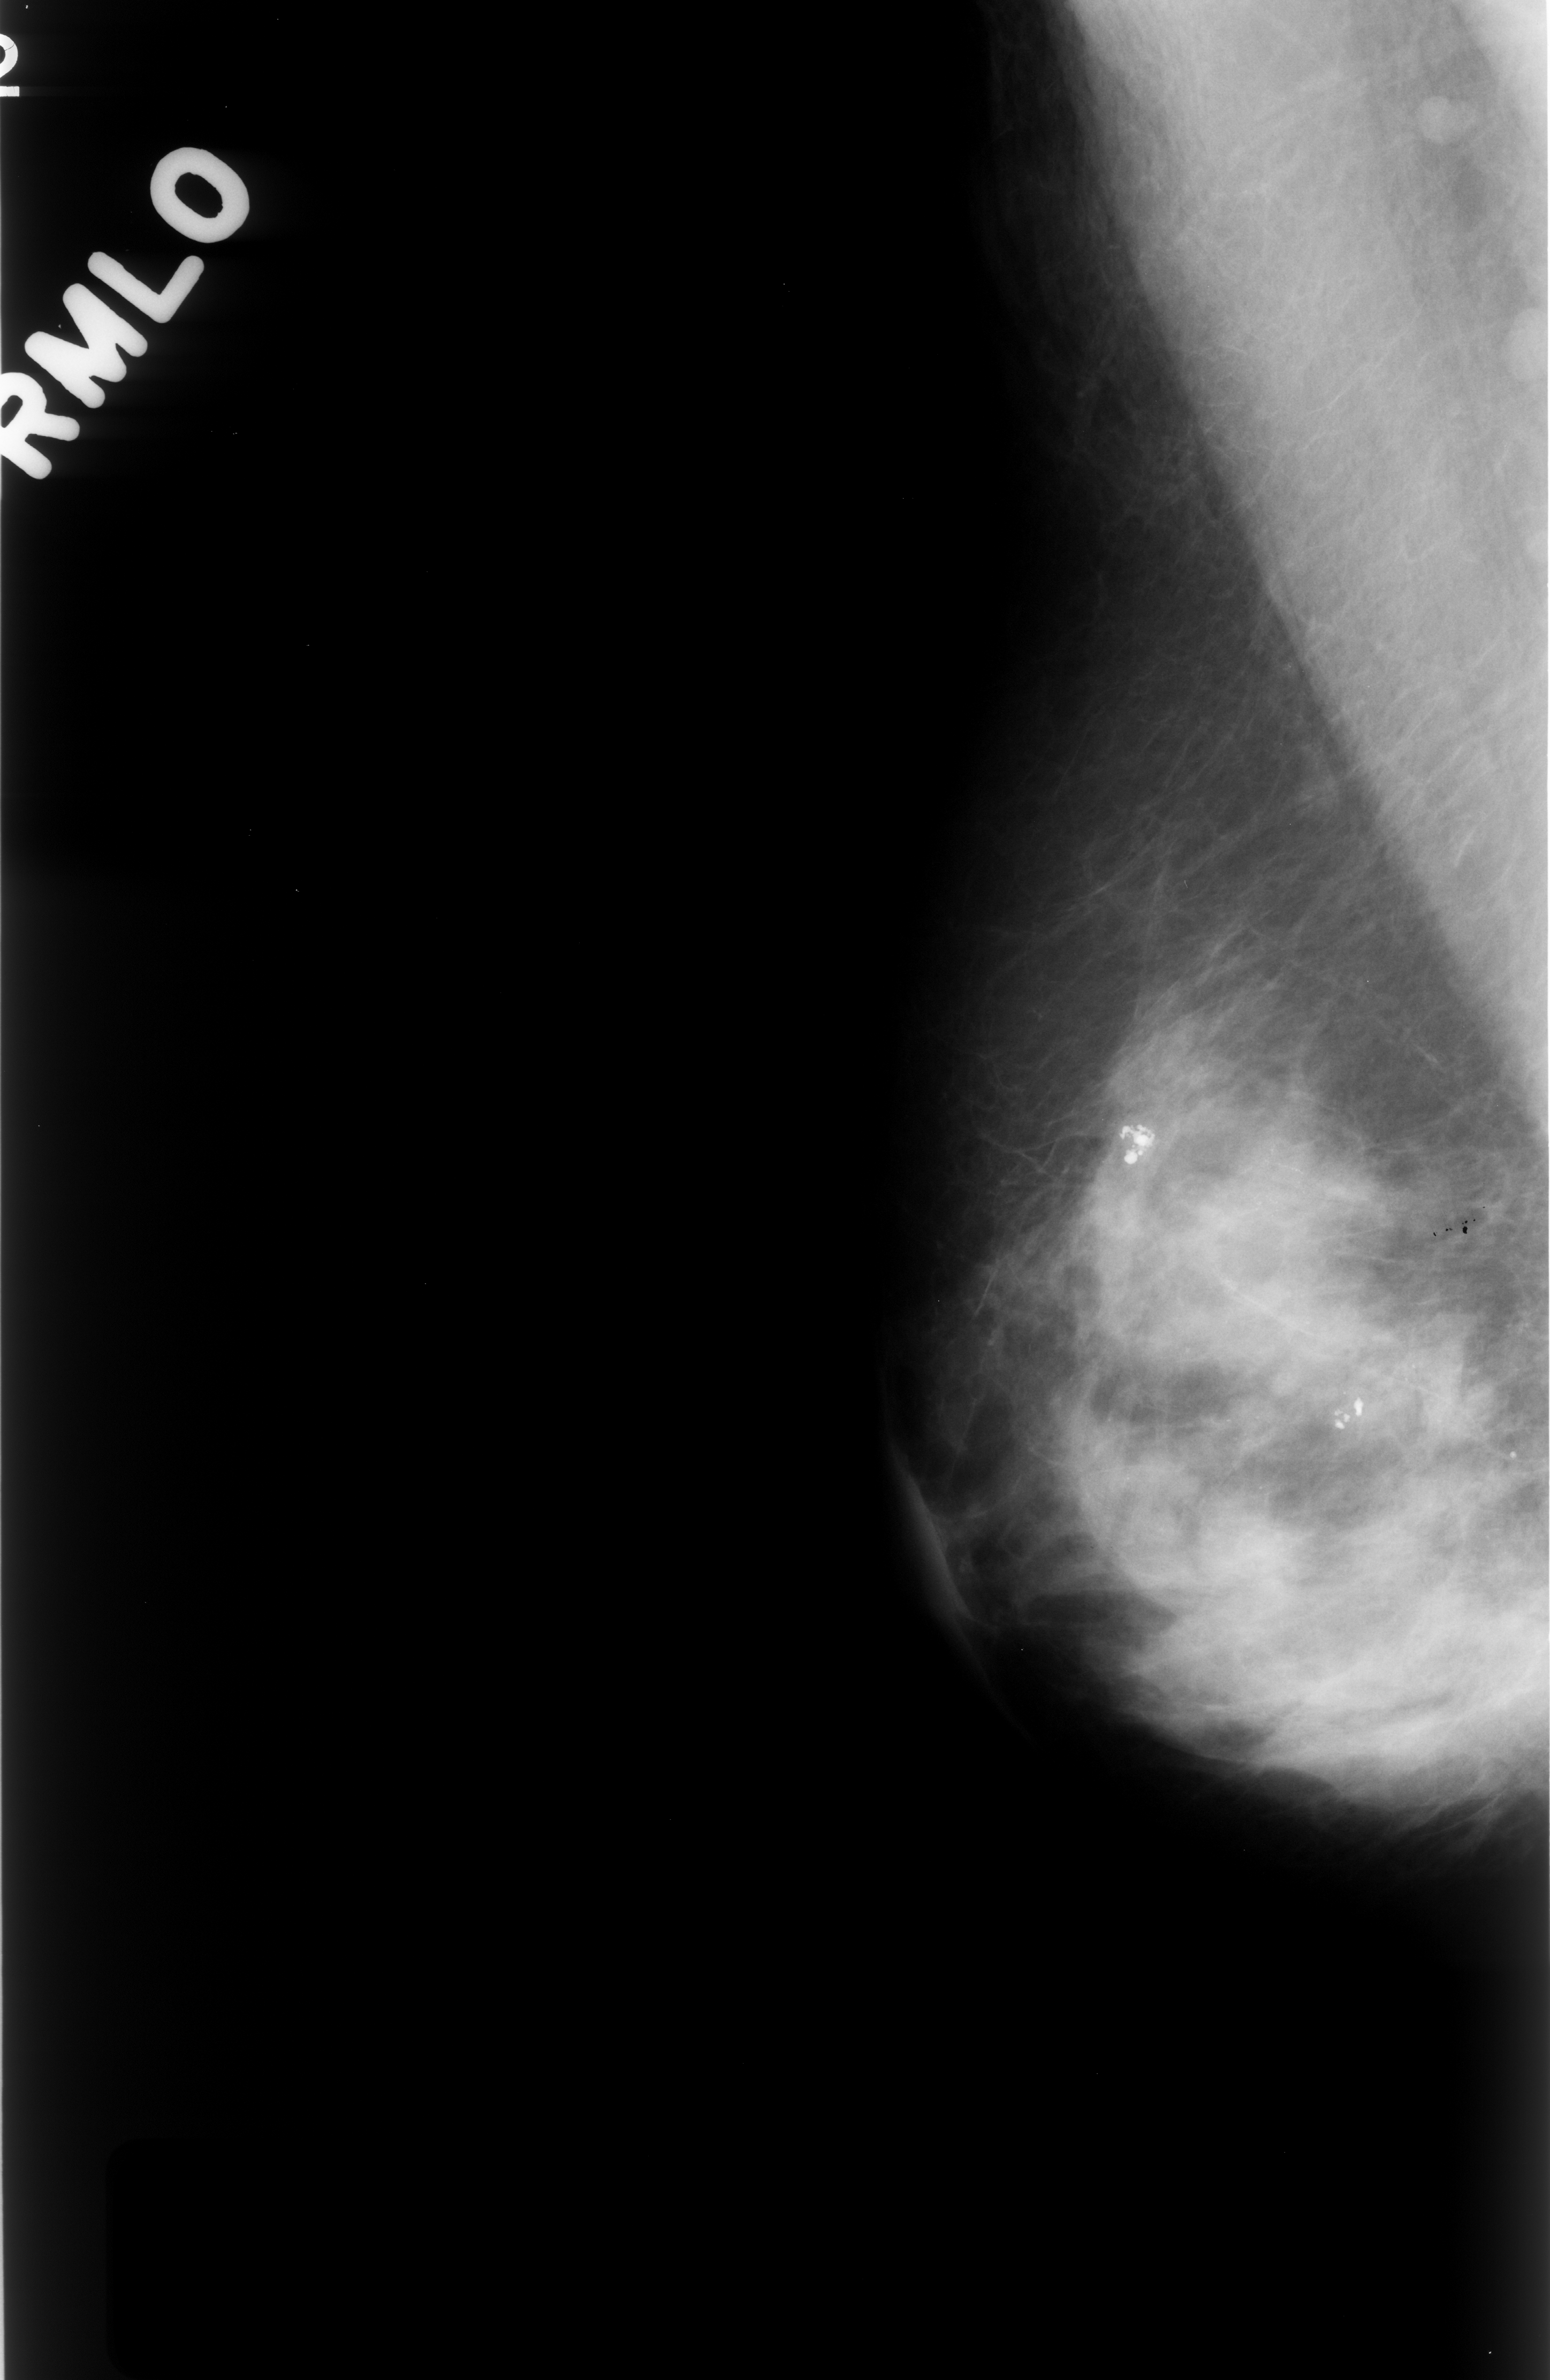
Digitized screen-film mammogram. Right breast. MLO view. Breast composition: heterogeneously dense (BI-RADS density category 3 of 4). 1550 × 2380 image matrix.
Expert-marked regions of interest on this film, with their recorded descriptors:
- calcifications, morphology amorphous, distribution clustered; BI-RADS assessment category 4; subtlety rating 2 on a 1 (subtle) to 5 (obvious) scale; pathology (as recorded): benign: bounding box [x1, y1, x2, y2] px = [1190, 1078, 1393, 1285]